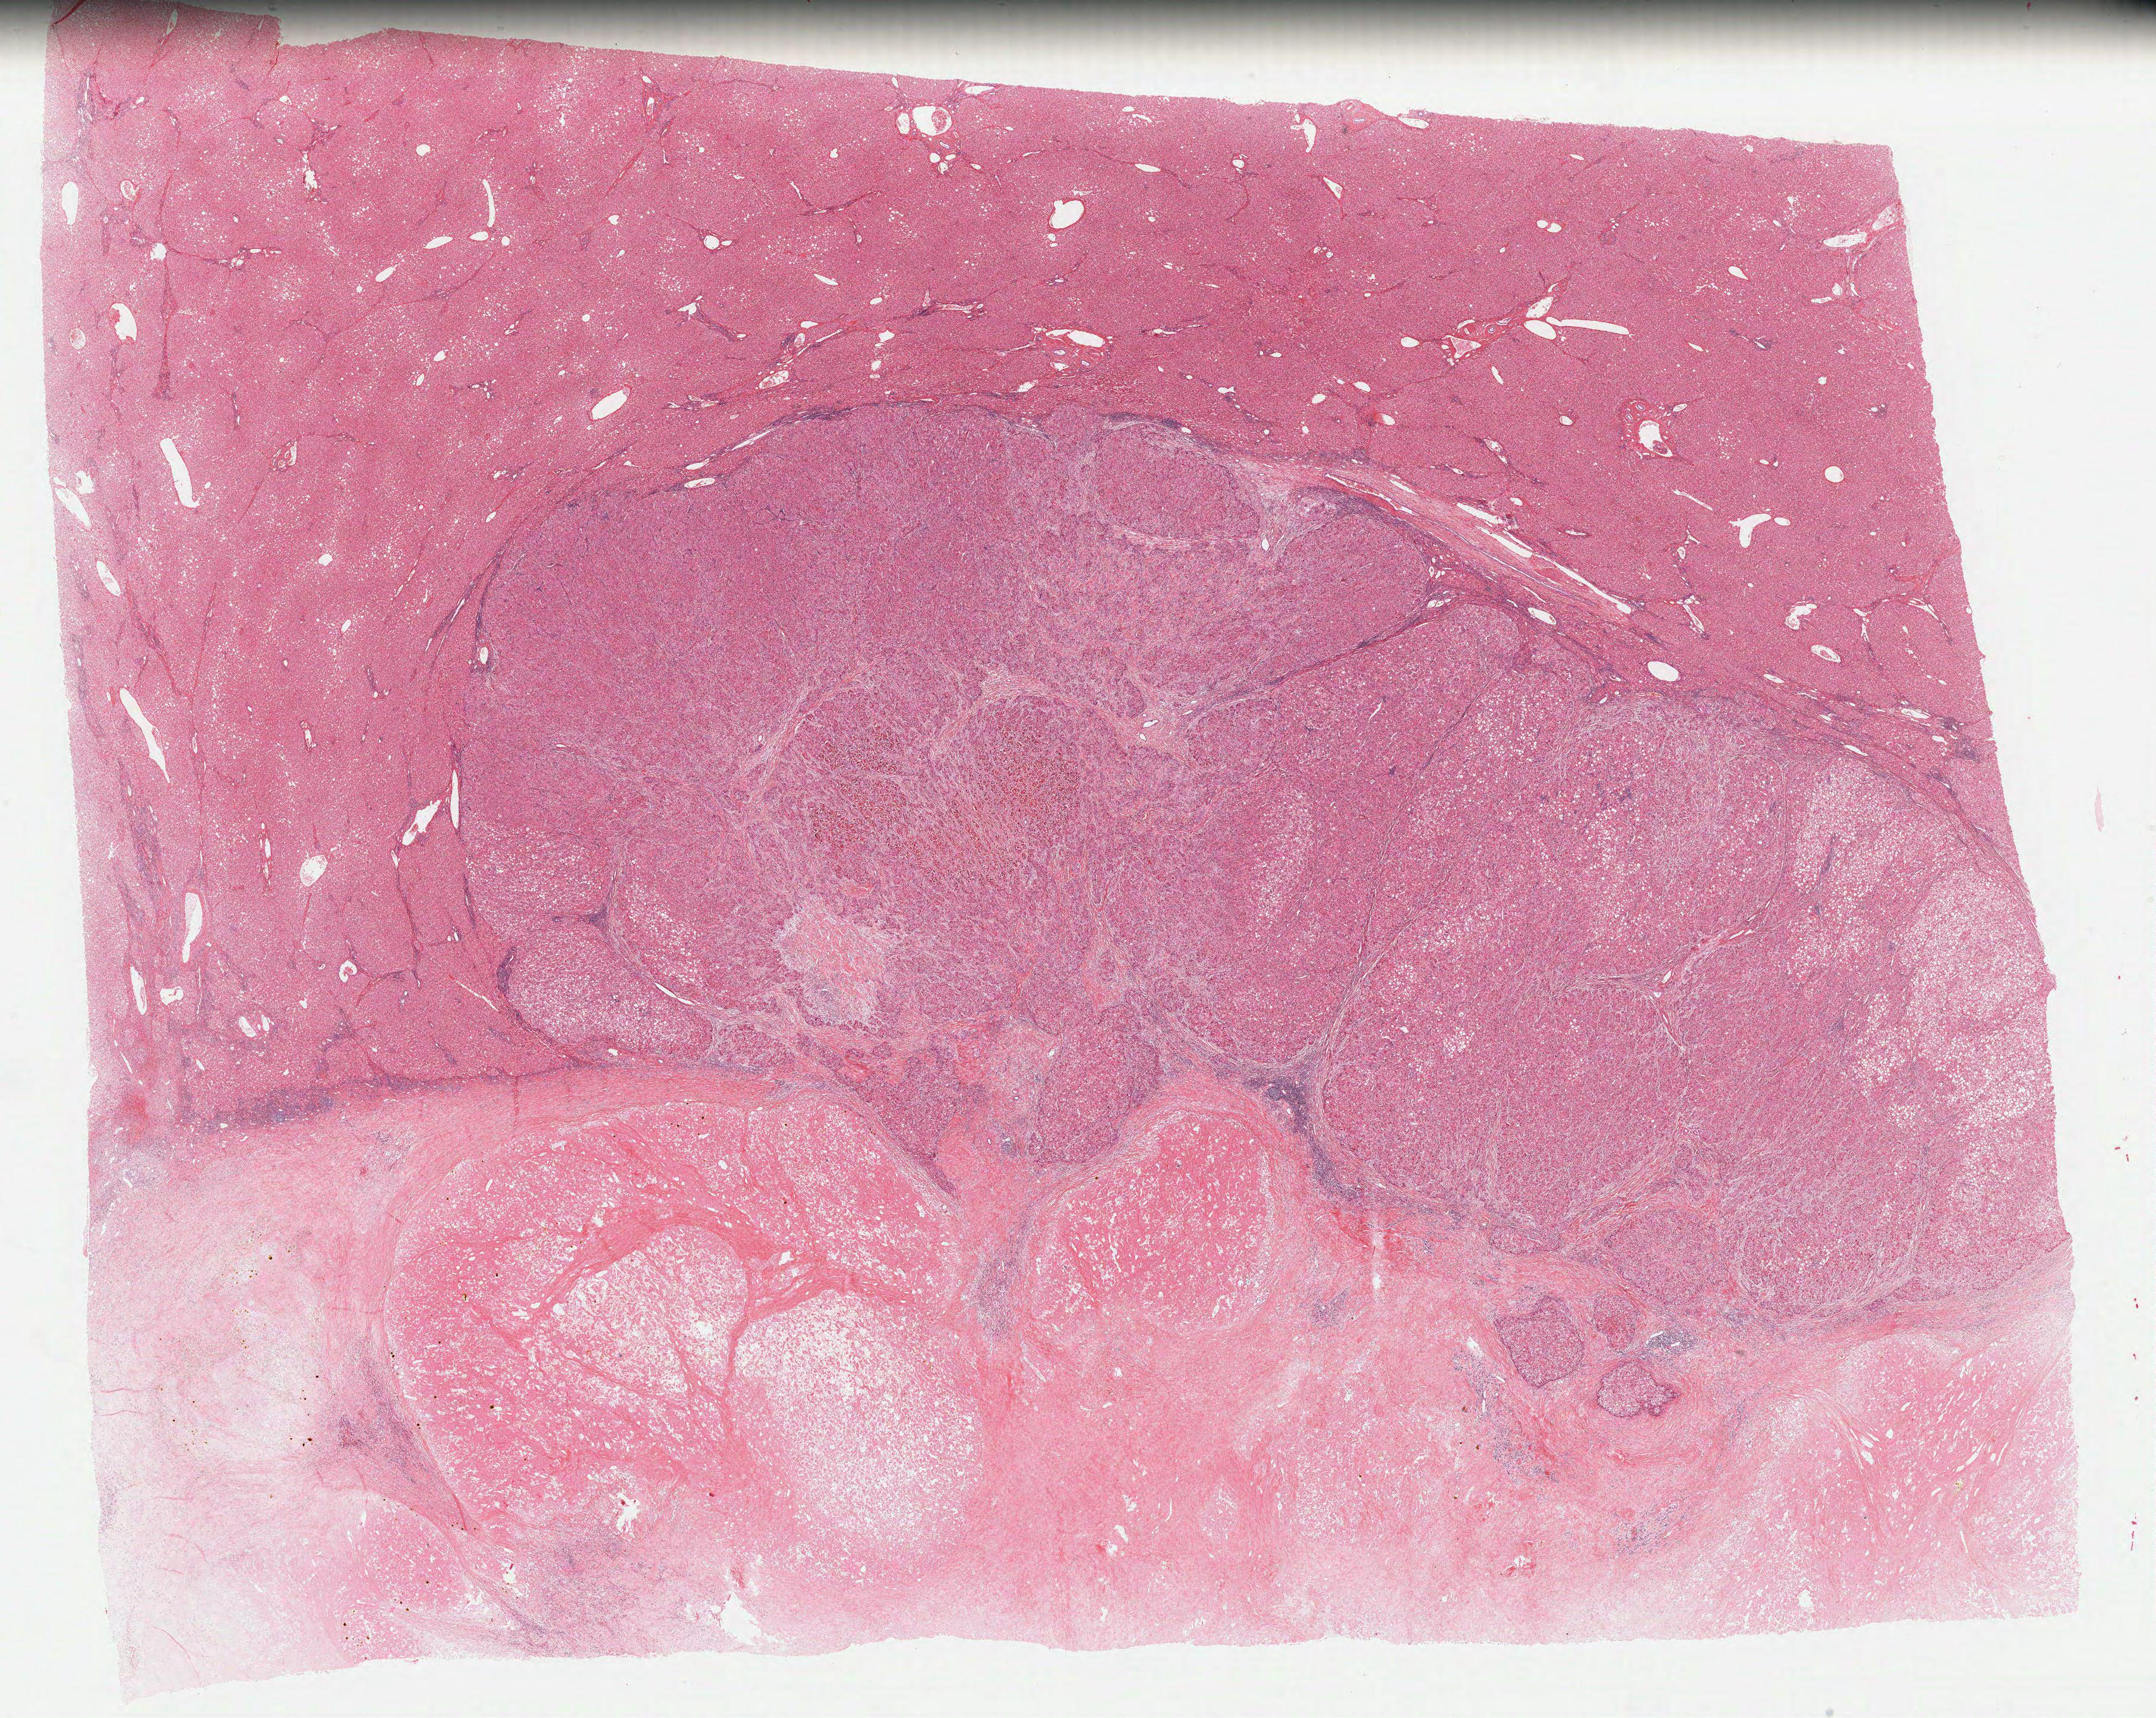
H&E-stained whole-slide image — a low-resolution overview of the entire scanned area, about 28.7 x 22.9 mm (acquisition: 40x scan), formalin-fixed paraffin-embedded (FFPE) diagnostic section, sample: primary tumour, liver. Male patient; age at initial diagnosis 54 years.
Histologic diagnosis: Hepatocellular carcinoma, NOS.